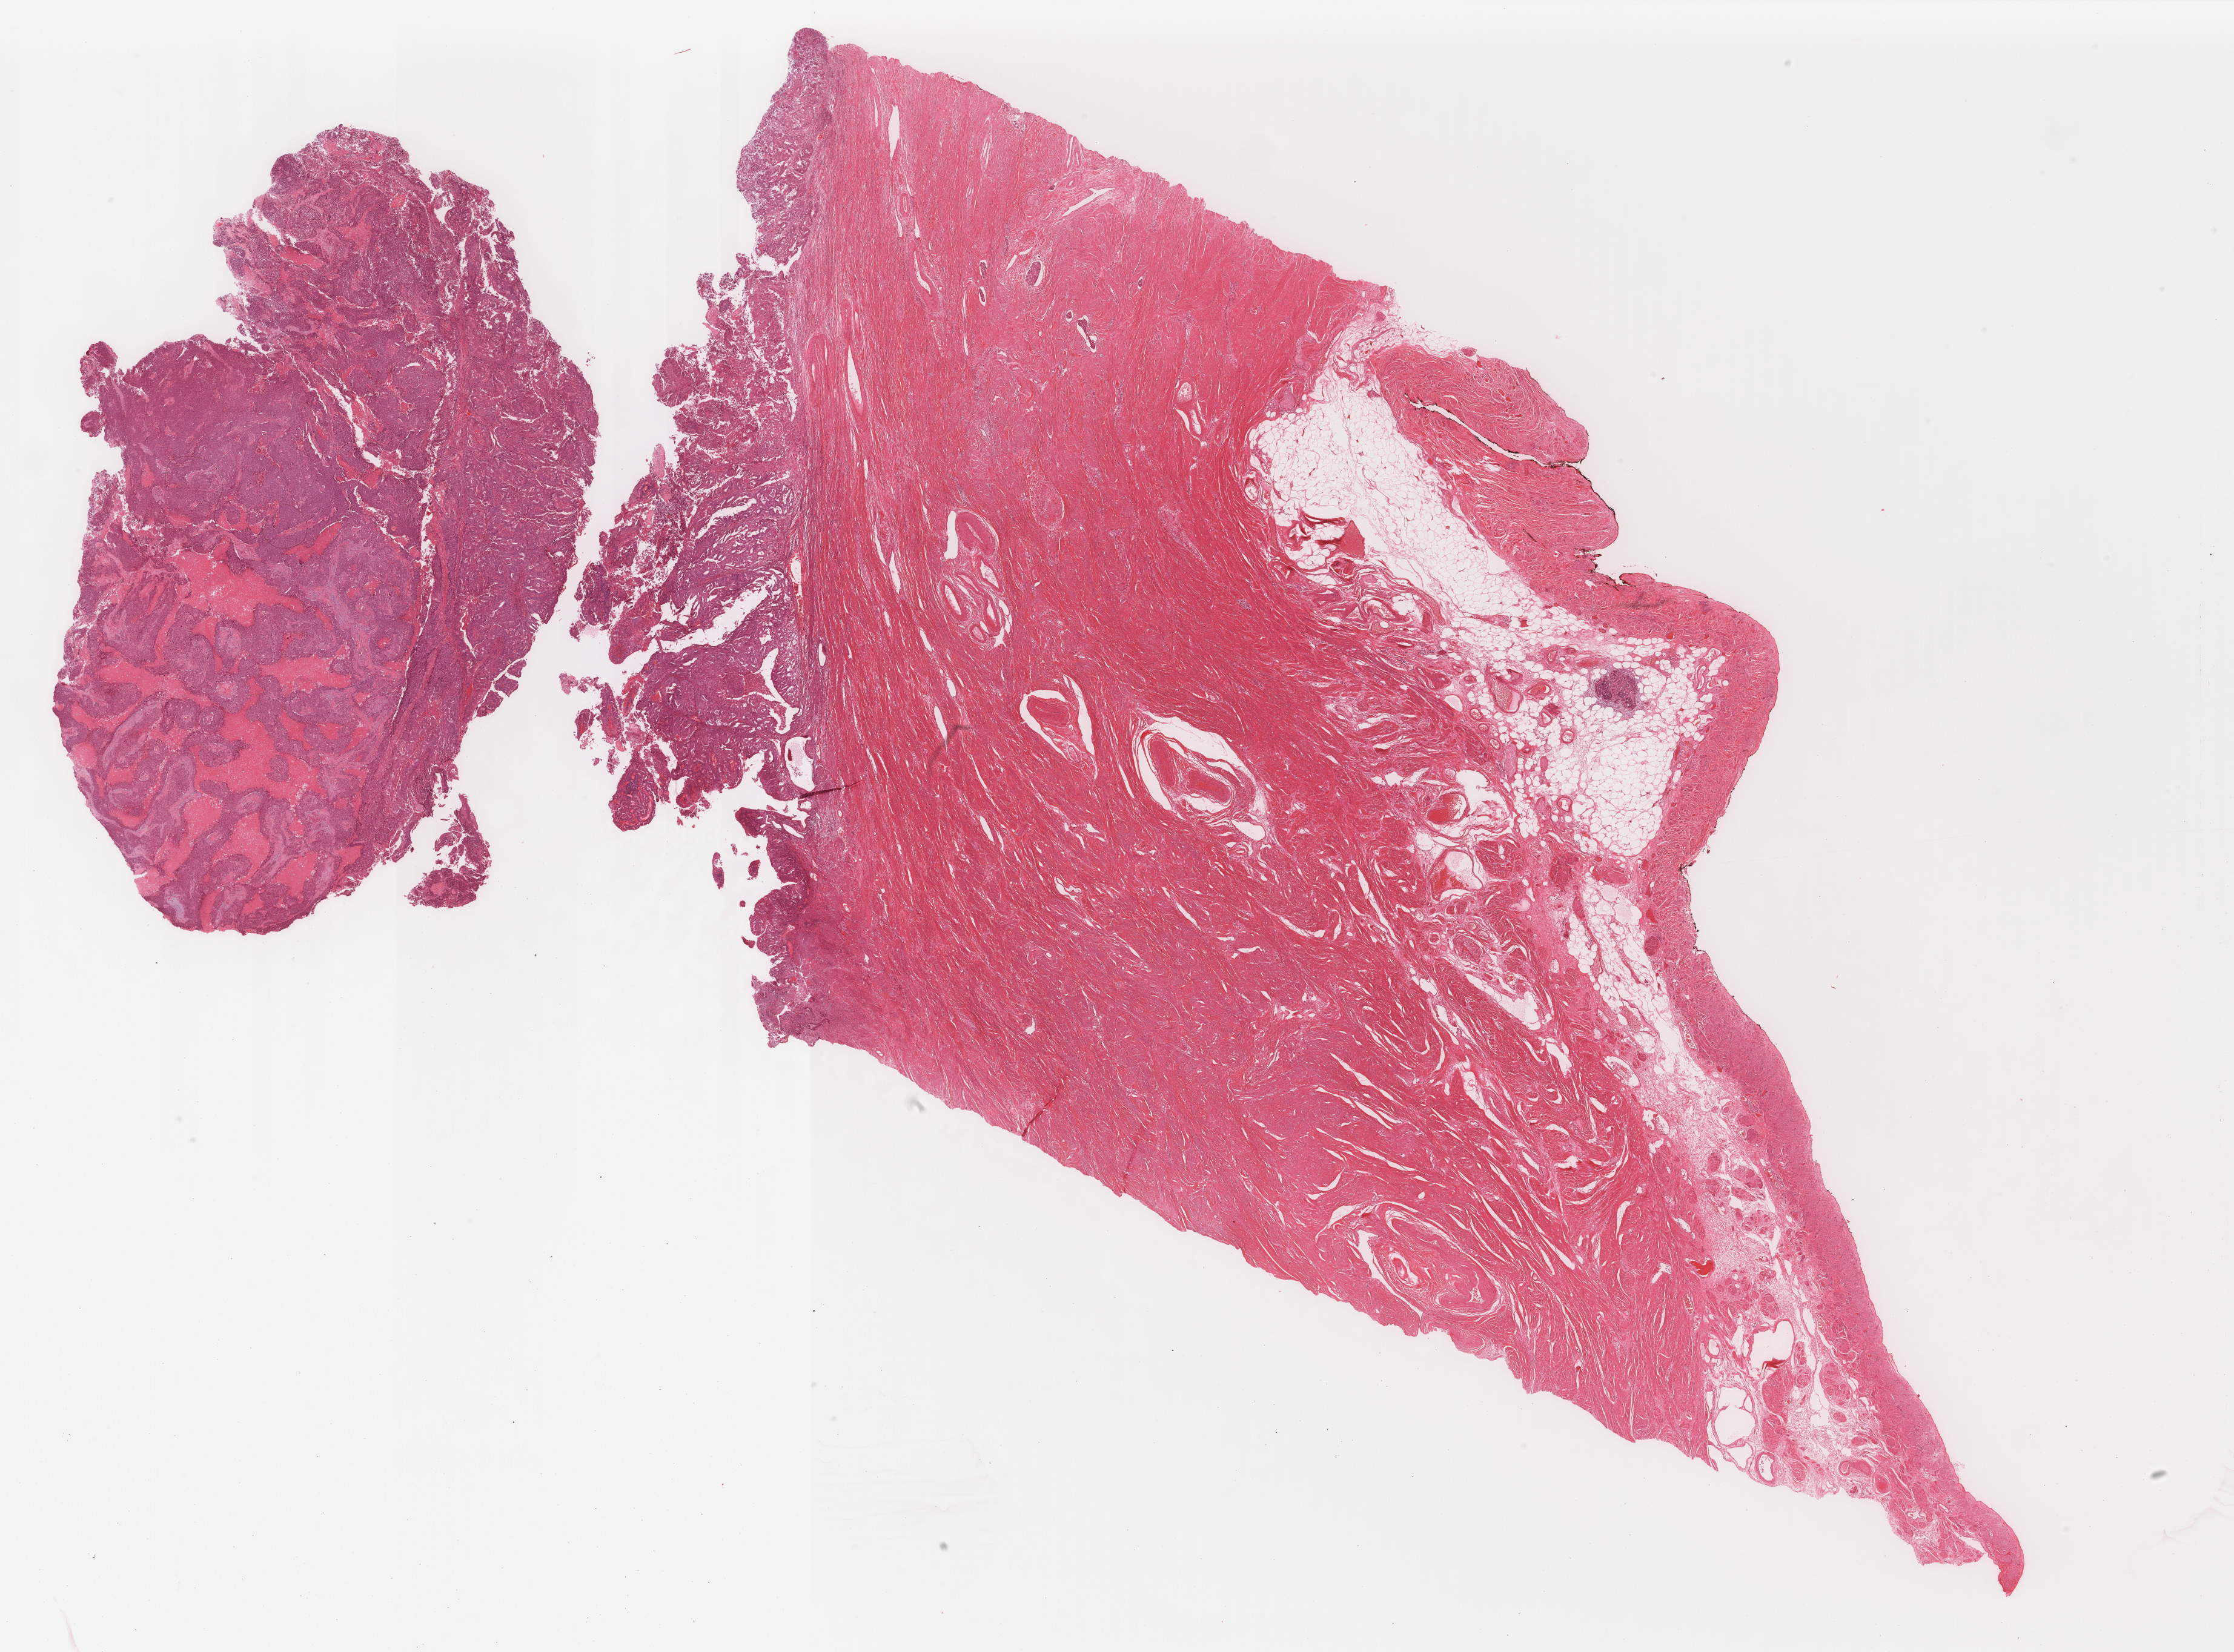
H&E-stained whole-slide image, whole scanned area (about 29.3 x 21.7 mm, from a 40x scan) shown as a low-resolution overview; FFPE section; primary tumour sample from the uterus. Patient: female, age at initial diagnosis 54 years. Histologic grade: G3 (poorly differentiated).
- pathologic diagnosis: Endometrioid adenocarcinoma, NOS (endometrium)
- FIGO stage: IIB